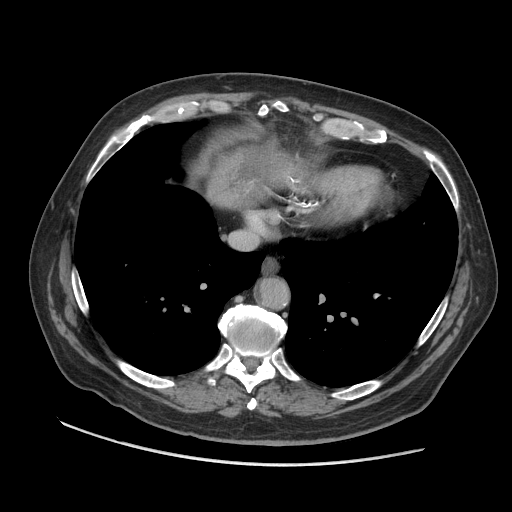
Contrast-enhanced abdominal CT (liver protocol), one axial slice. Slice 95 of 109 in the series (ordered by position). 140 kVp. Soft-tissue window (W 400 / L 40 HU). 2.5 mm slice thickness. 512 × 512 image matrix, field of view 420 × 420 mm. Case-level facts recorded for this patient, not image findings: diagnosis: hepatocellular carcinoma (patient treated with transarterial chemoembolisation; whether this scan precedes or follows treatment is not stated here); TNM stage (as recorded): Stage-I; Child-Pugh class: A; tumour nodularity: uninodular.
Structures marked on this image (semi-automatically segmented with operator editing):
- mass: bounding box <207,144,282,208> (left, top, right, bottom; pixels)